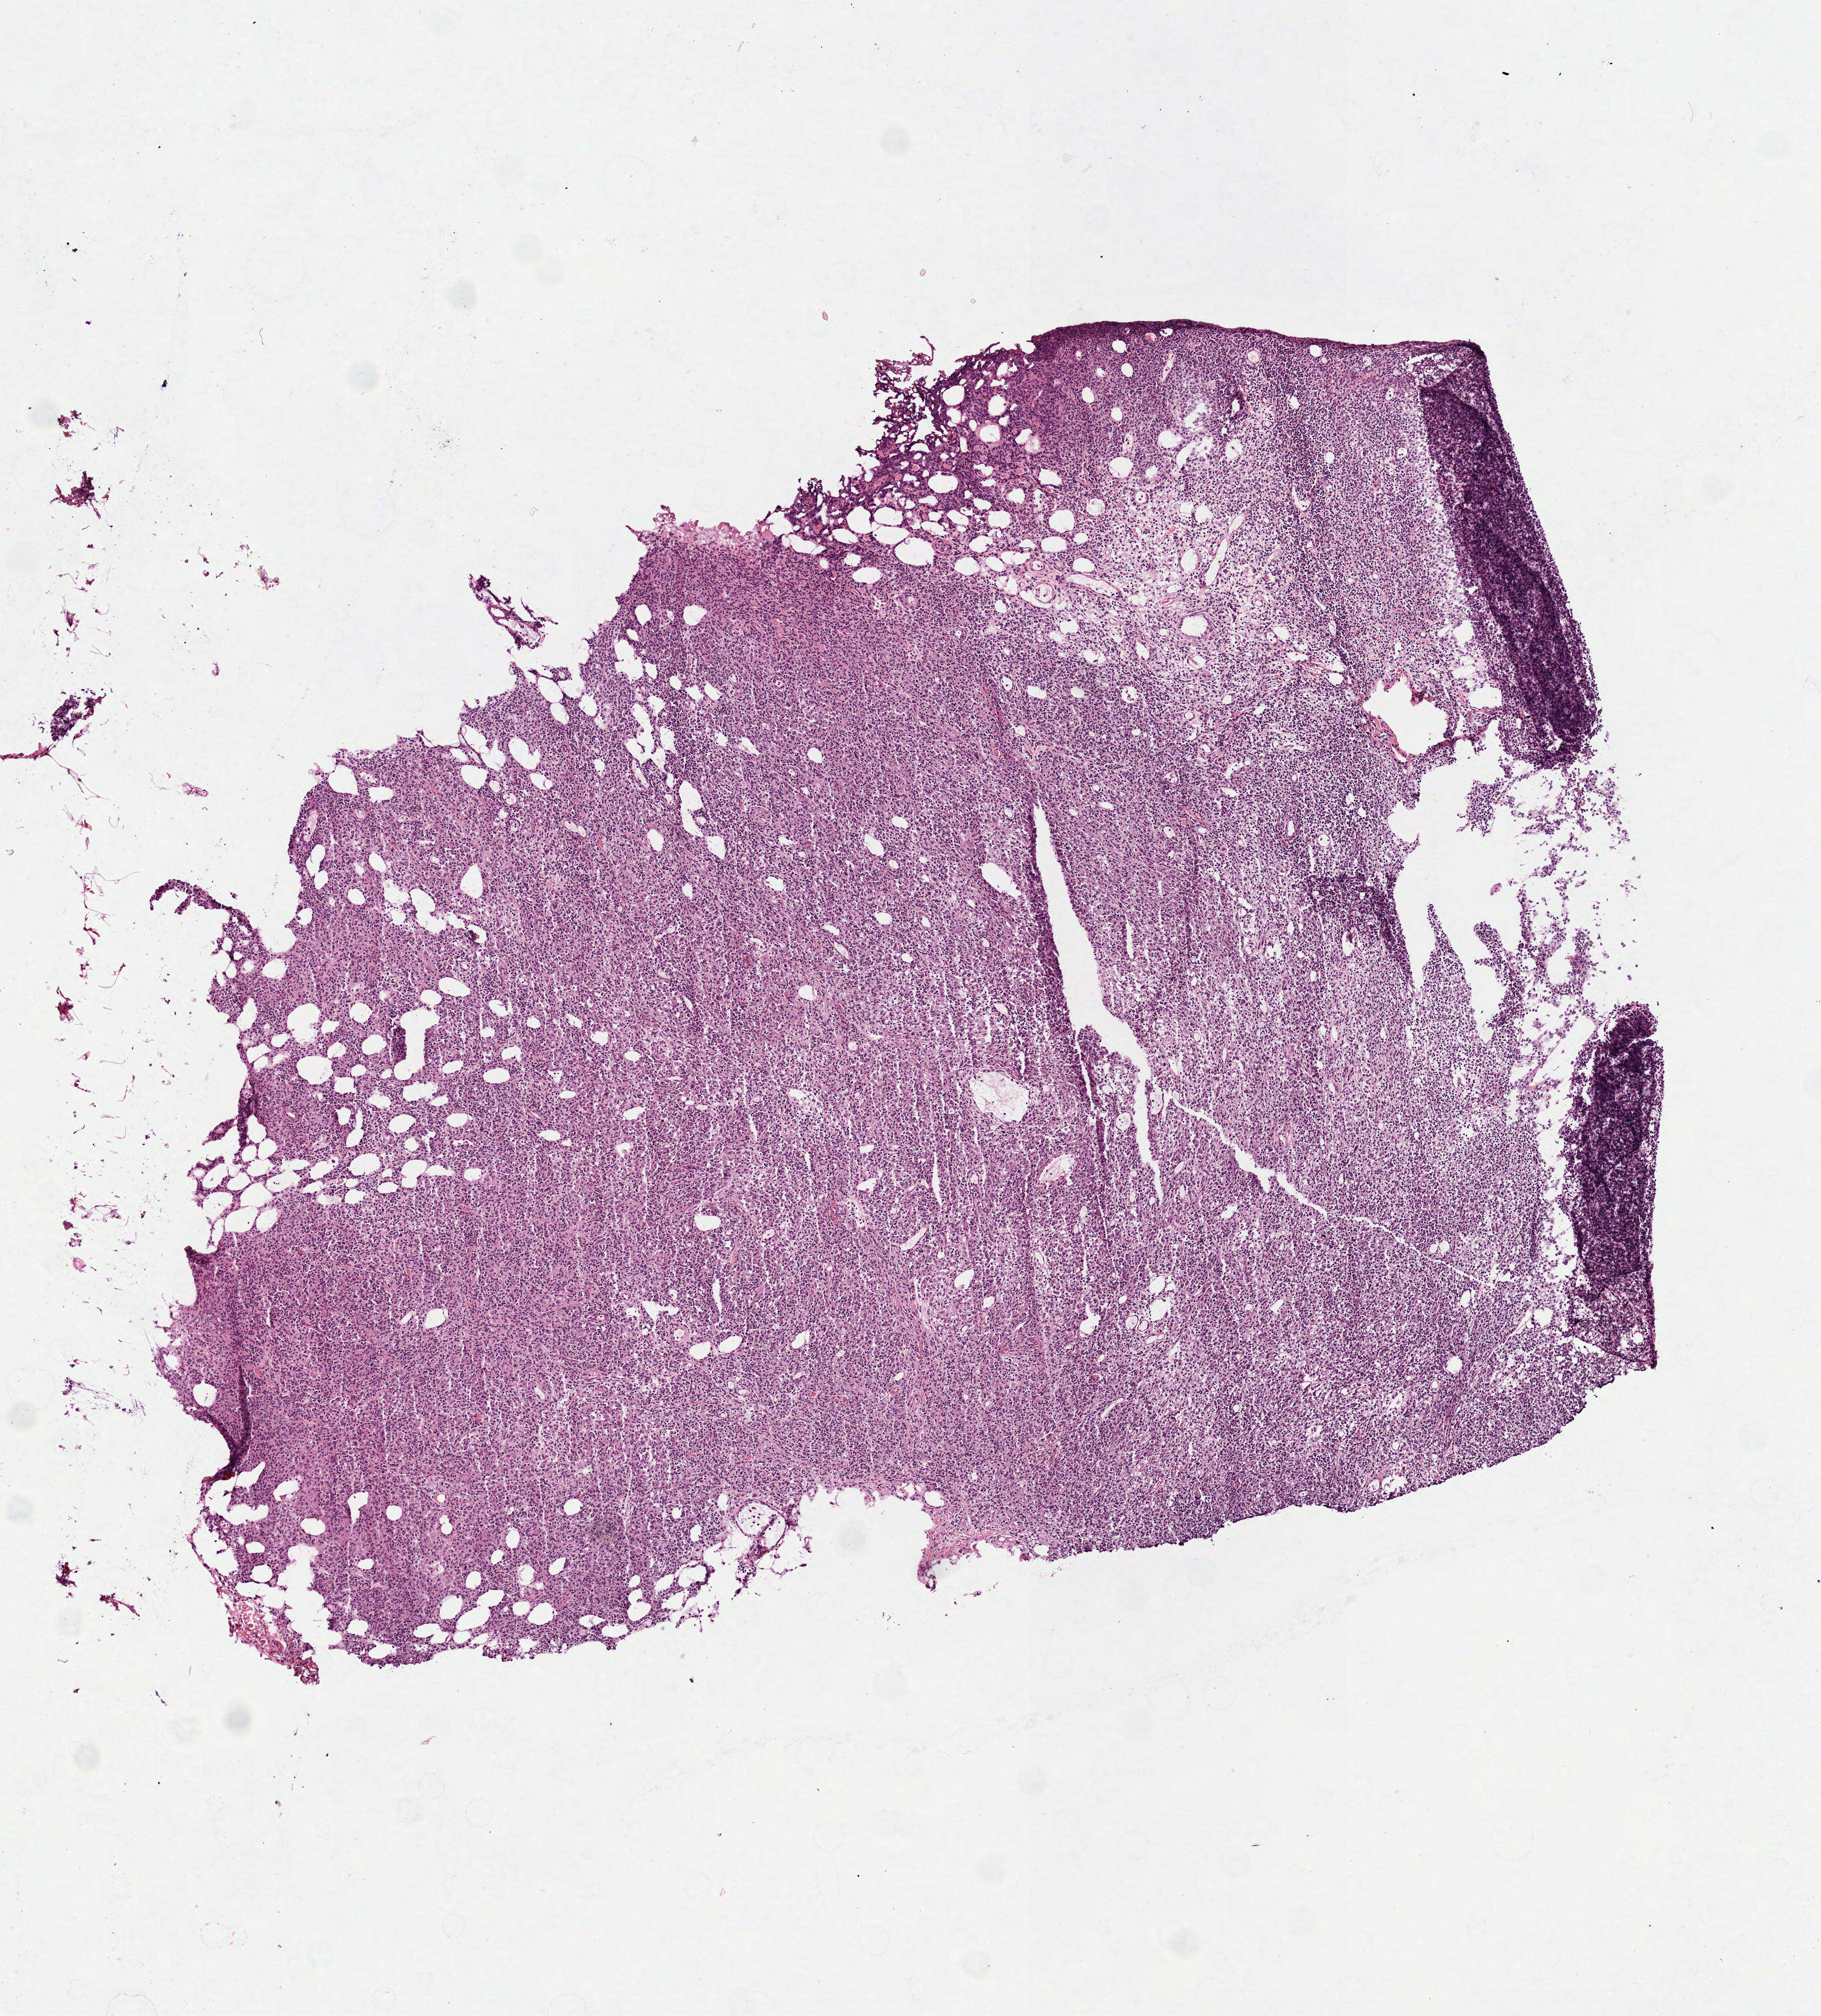
Digitized H&E tissue section (whole slide) — whole scanned area (about 5.6 x 6.2 mm, acquisition: 40x scan) shown as a low-resolution overview. Frozen section. Sample: primary tumour, lymphoid tissue. Male patient; age at initial diagnosis 52 years. Pathologist review of this section (percent, as recorded): tumour cells 95%, tumour nuclei 85%, normal cells 0%, stromal cells 5%, necrosis 0%.
Histologic diagnosis: Diffuse large B-cell lymphoma, NOS.